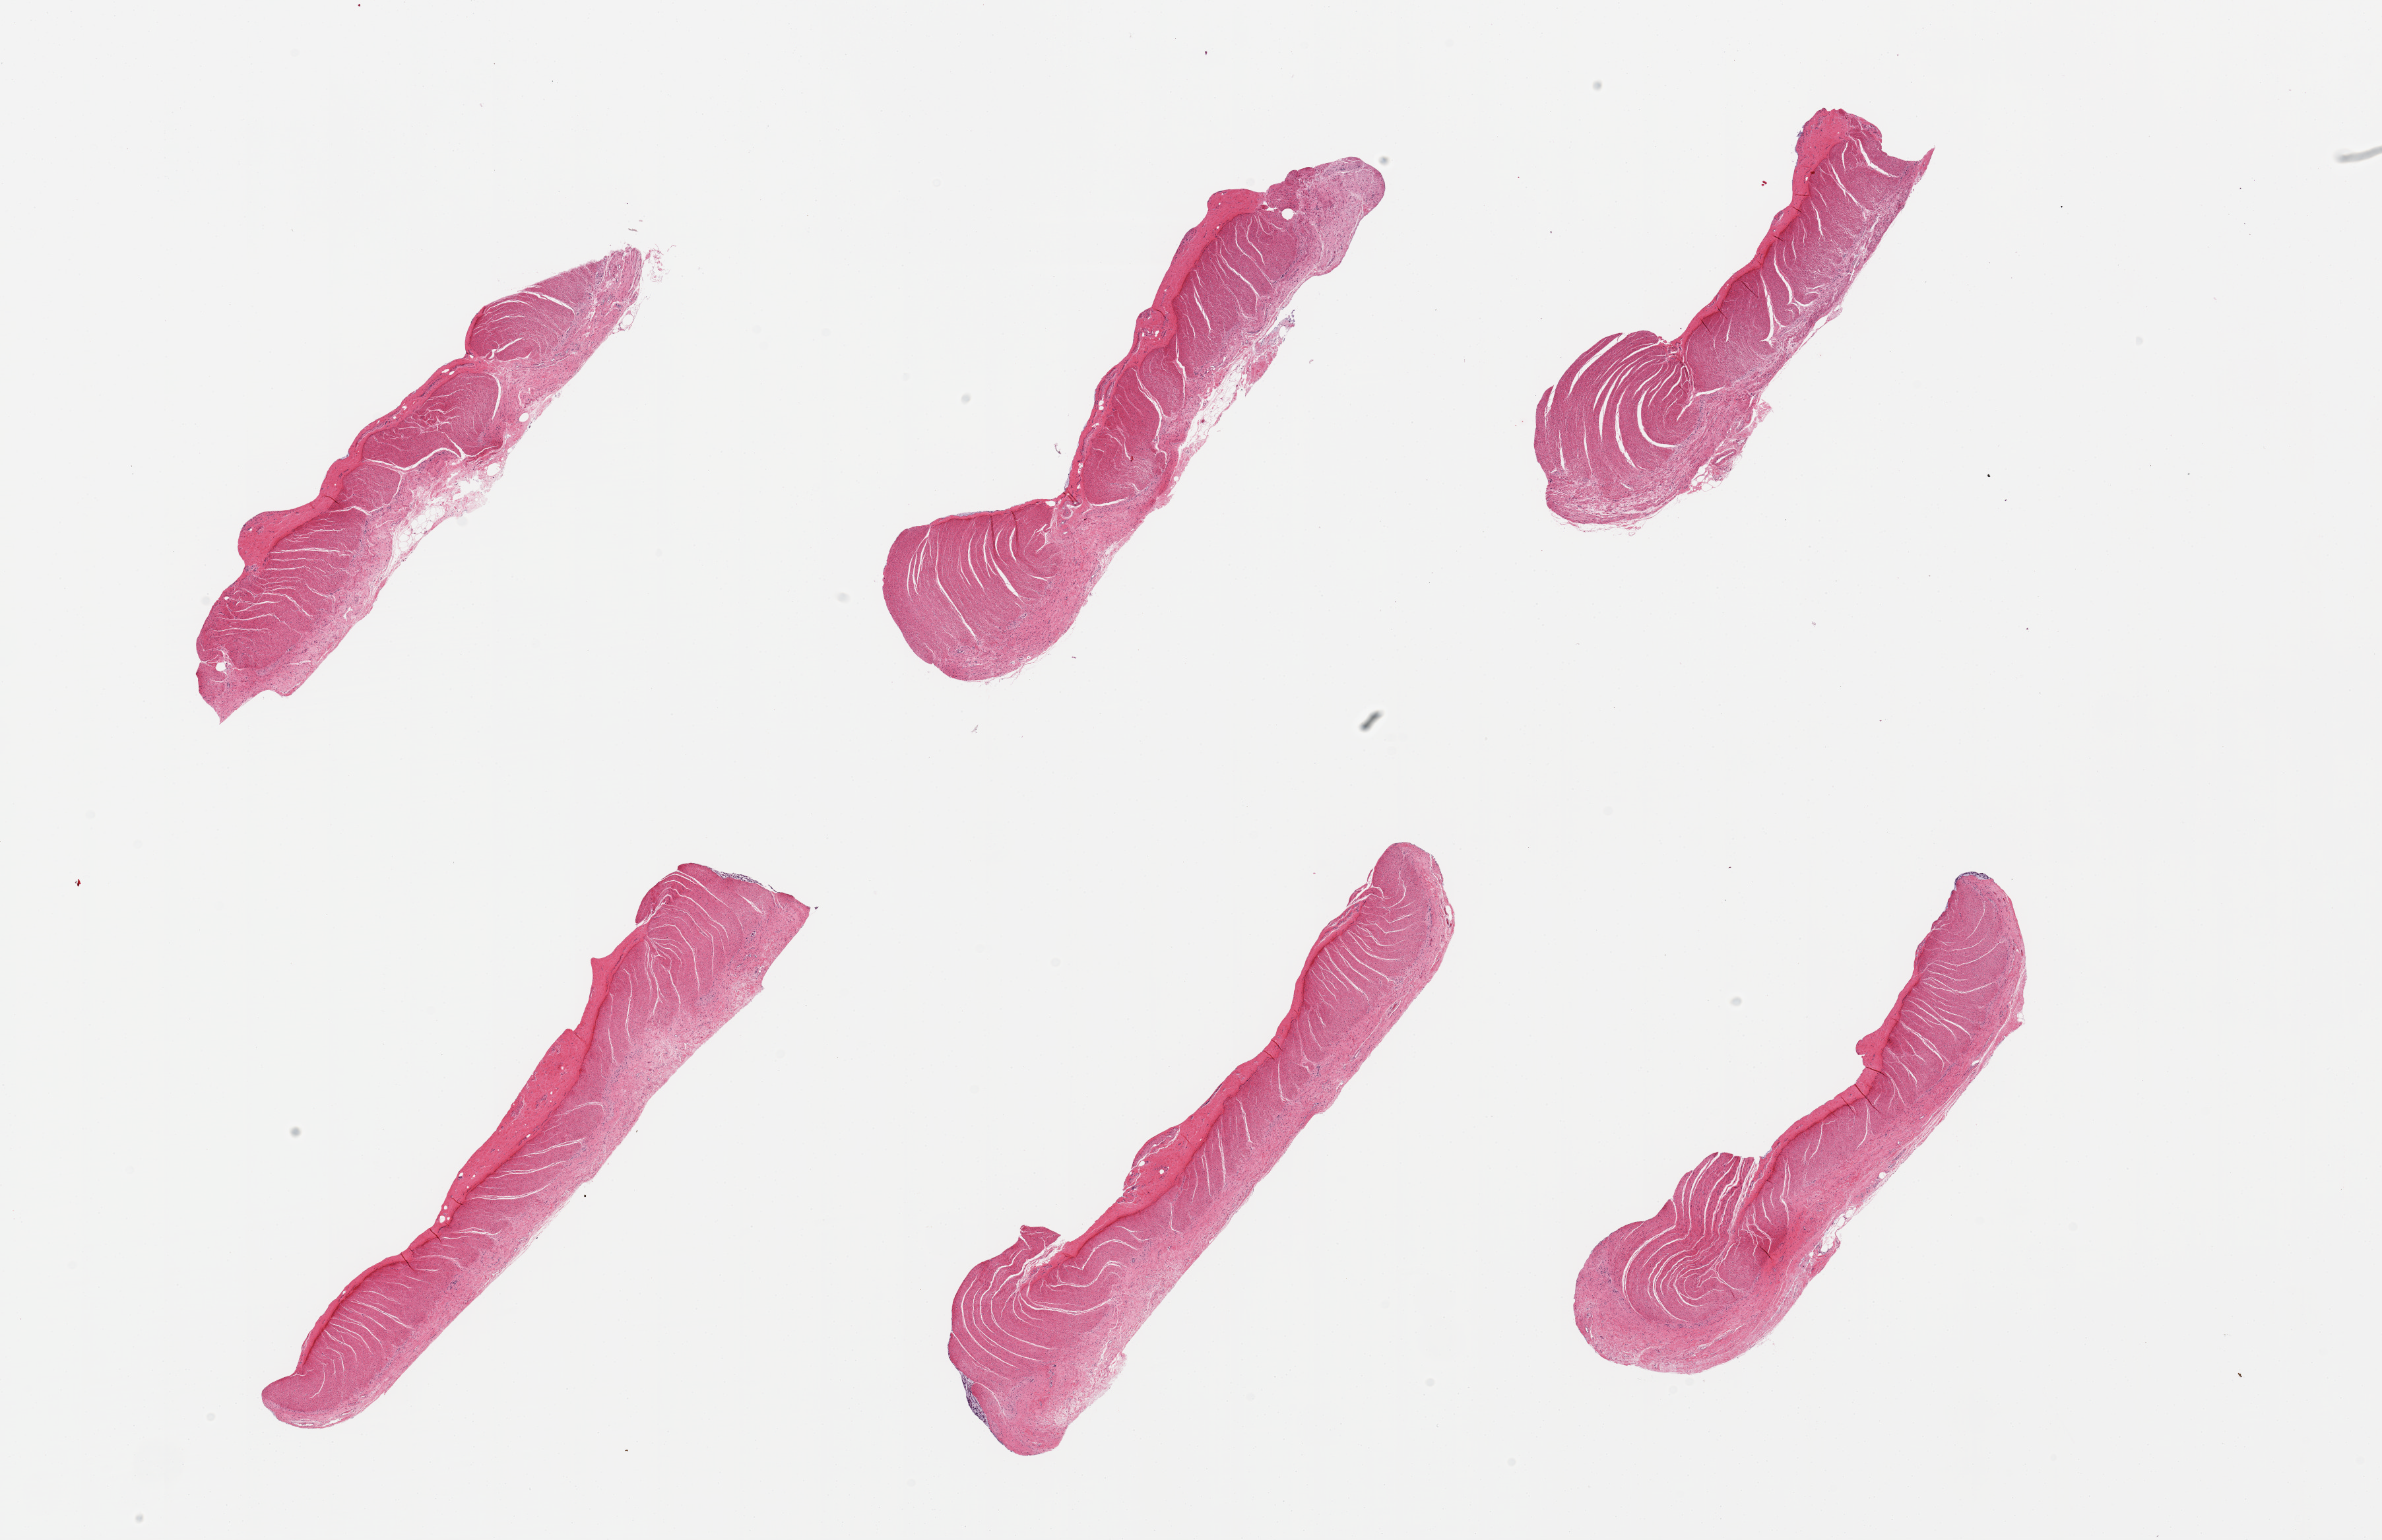
Haematoxylin and eosin whole-slide image, brightfield, low-resolution overview of the scanned area, about 28.5 x 18.5 mm (slide scanned at 20x). PAXgene-fixed, paraffin-embedded tissue. Sampled site (target tissue): sigmoid colon. Tissue donor sample. Donor sex: male.
Reviewer comment on this tissue sample: 6 pieces; well trimmed.